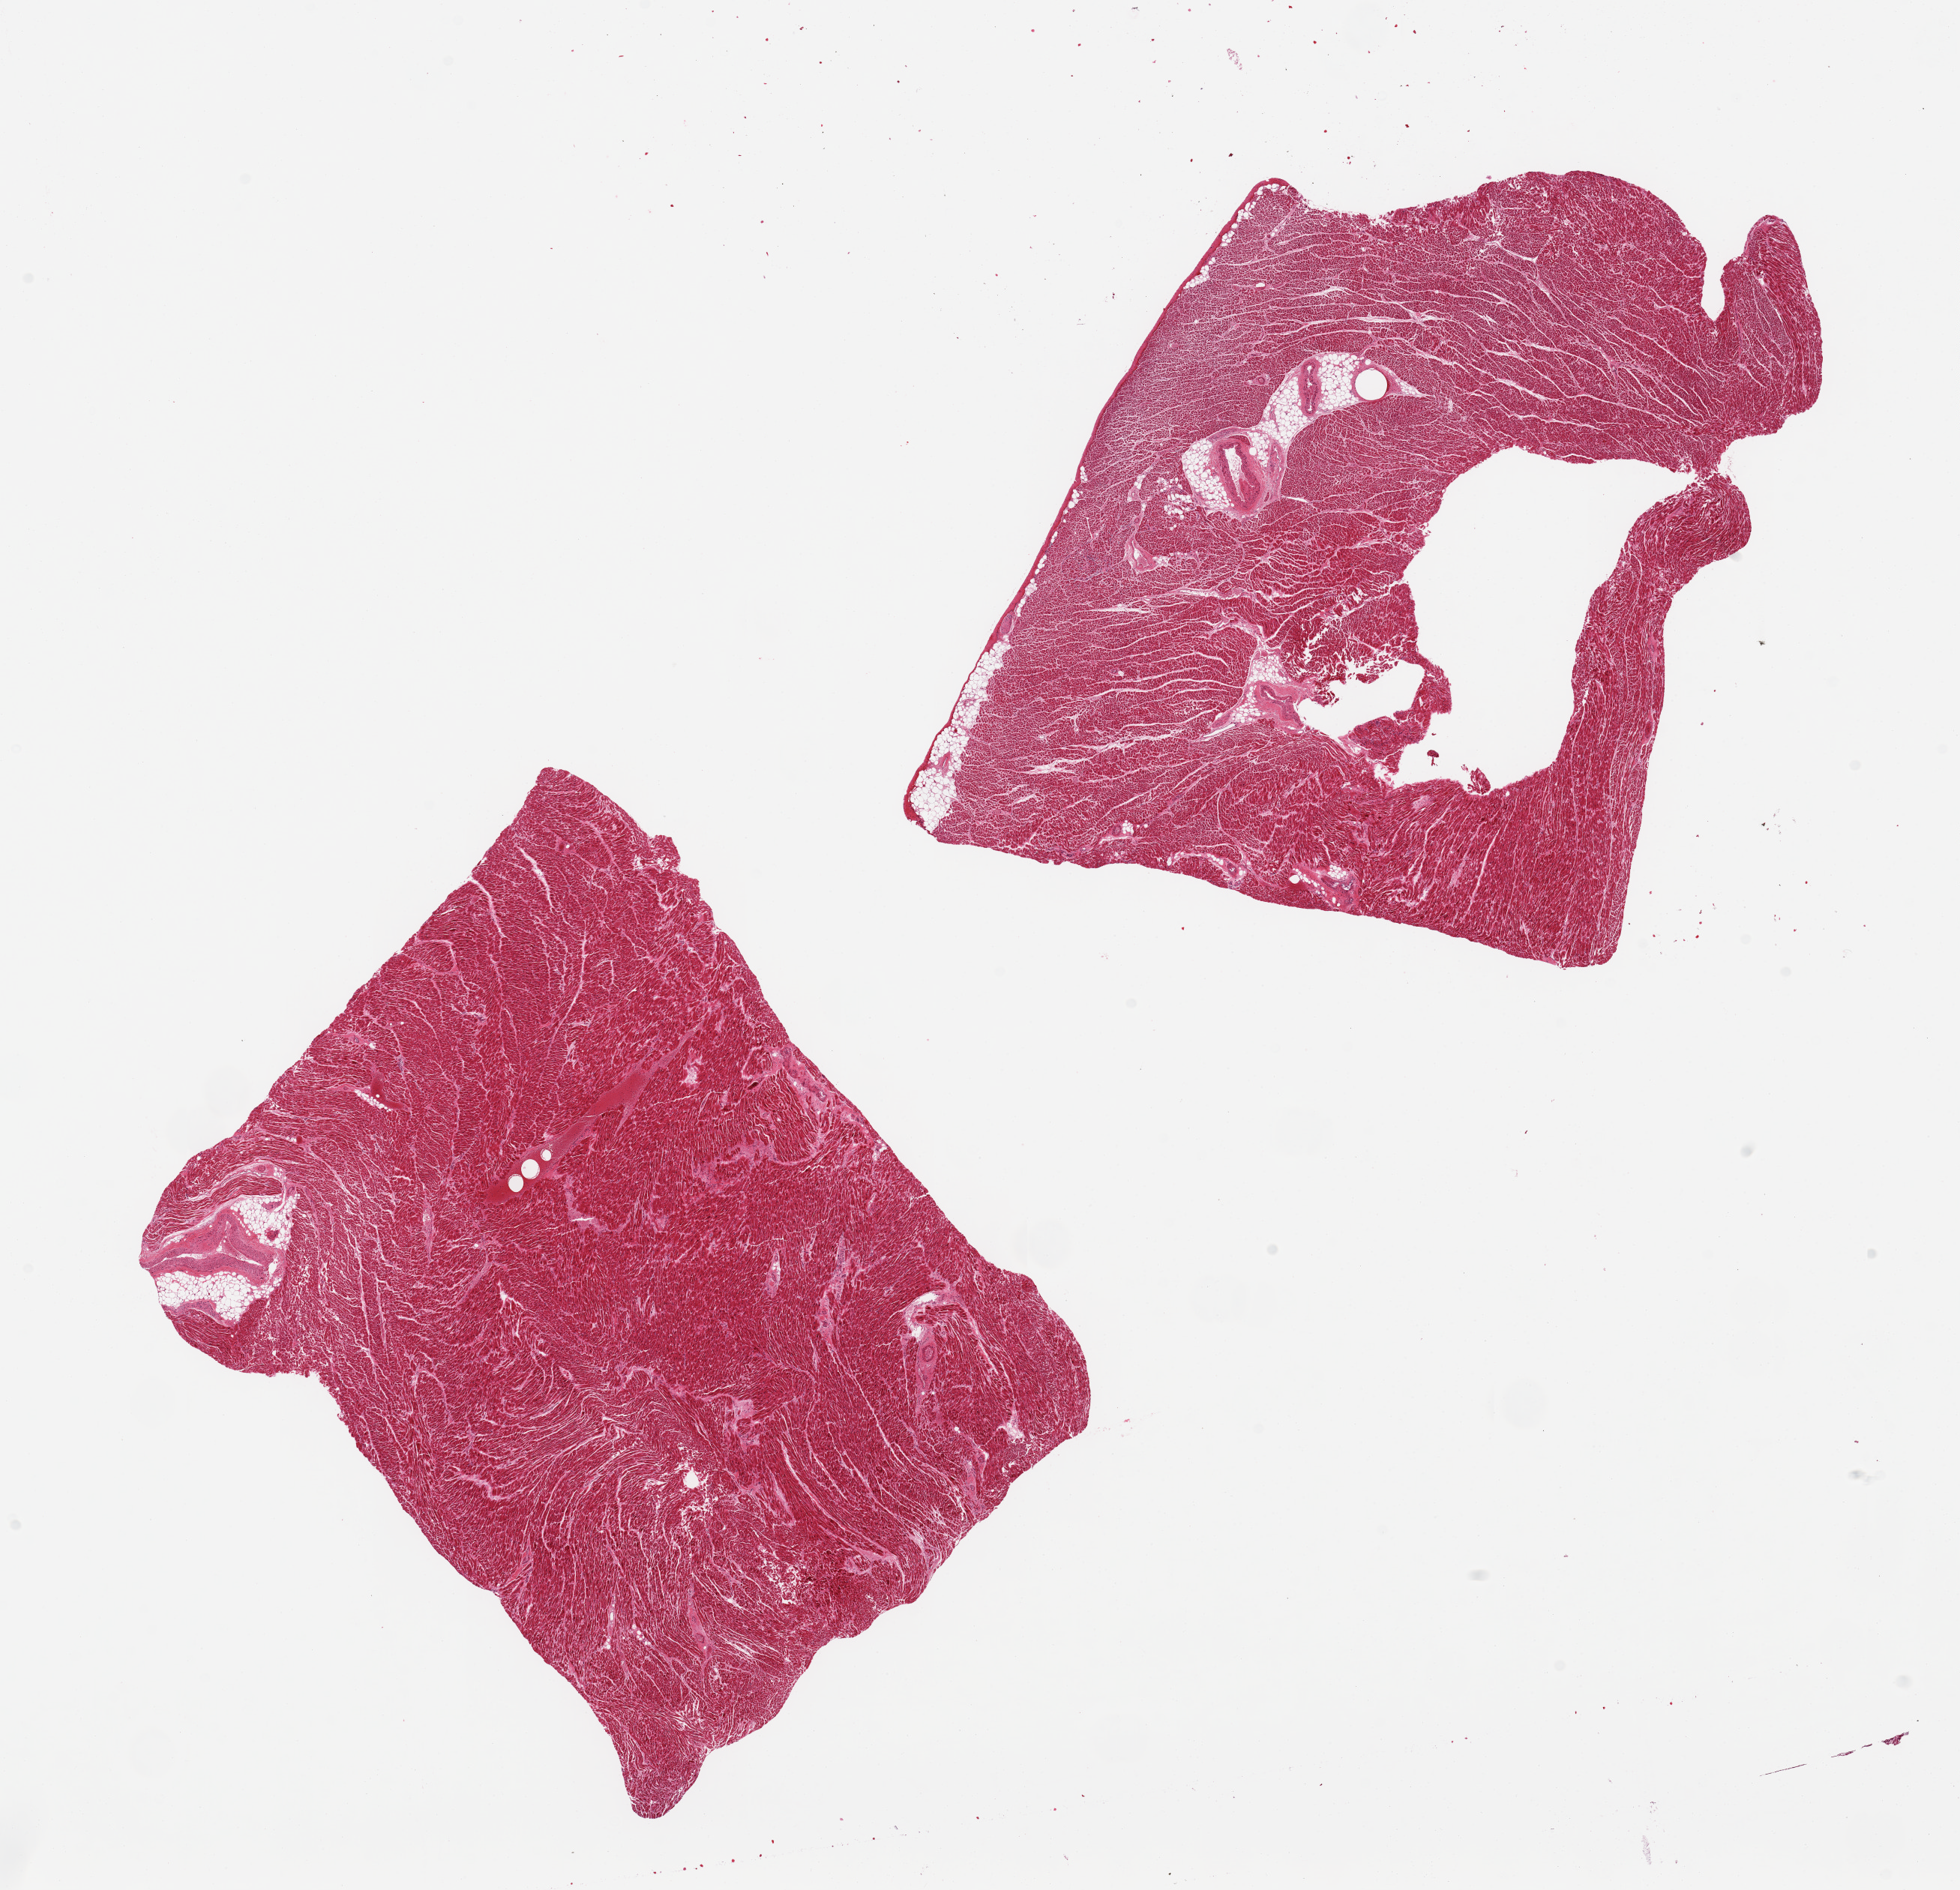
Digitized H&E-stained section — low-resolution overview of the scanned area, about 20.7 x 19.9 mm (slide scanned at 20x). PAXgene-fixed paraffin-embedded (PFPE) section. Section of heart (target tissue). Donor tissue sample. Female donor.
- review note (as recorded): 2 pieces, mild interstitial fibrosis/chronic ischemic changes